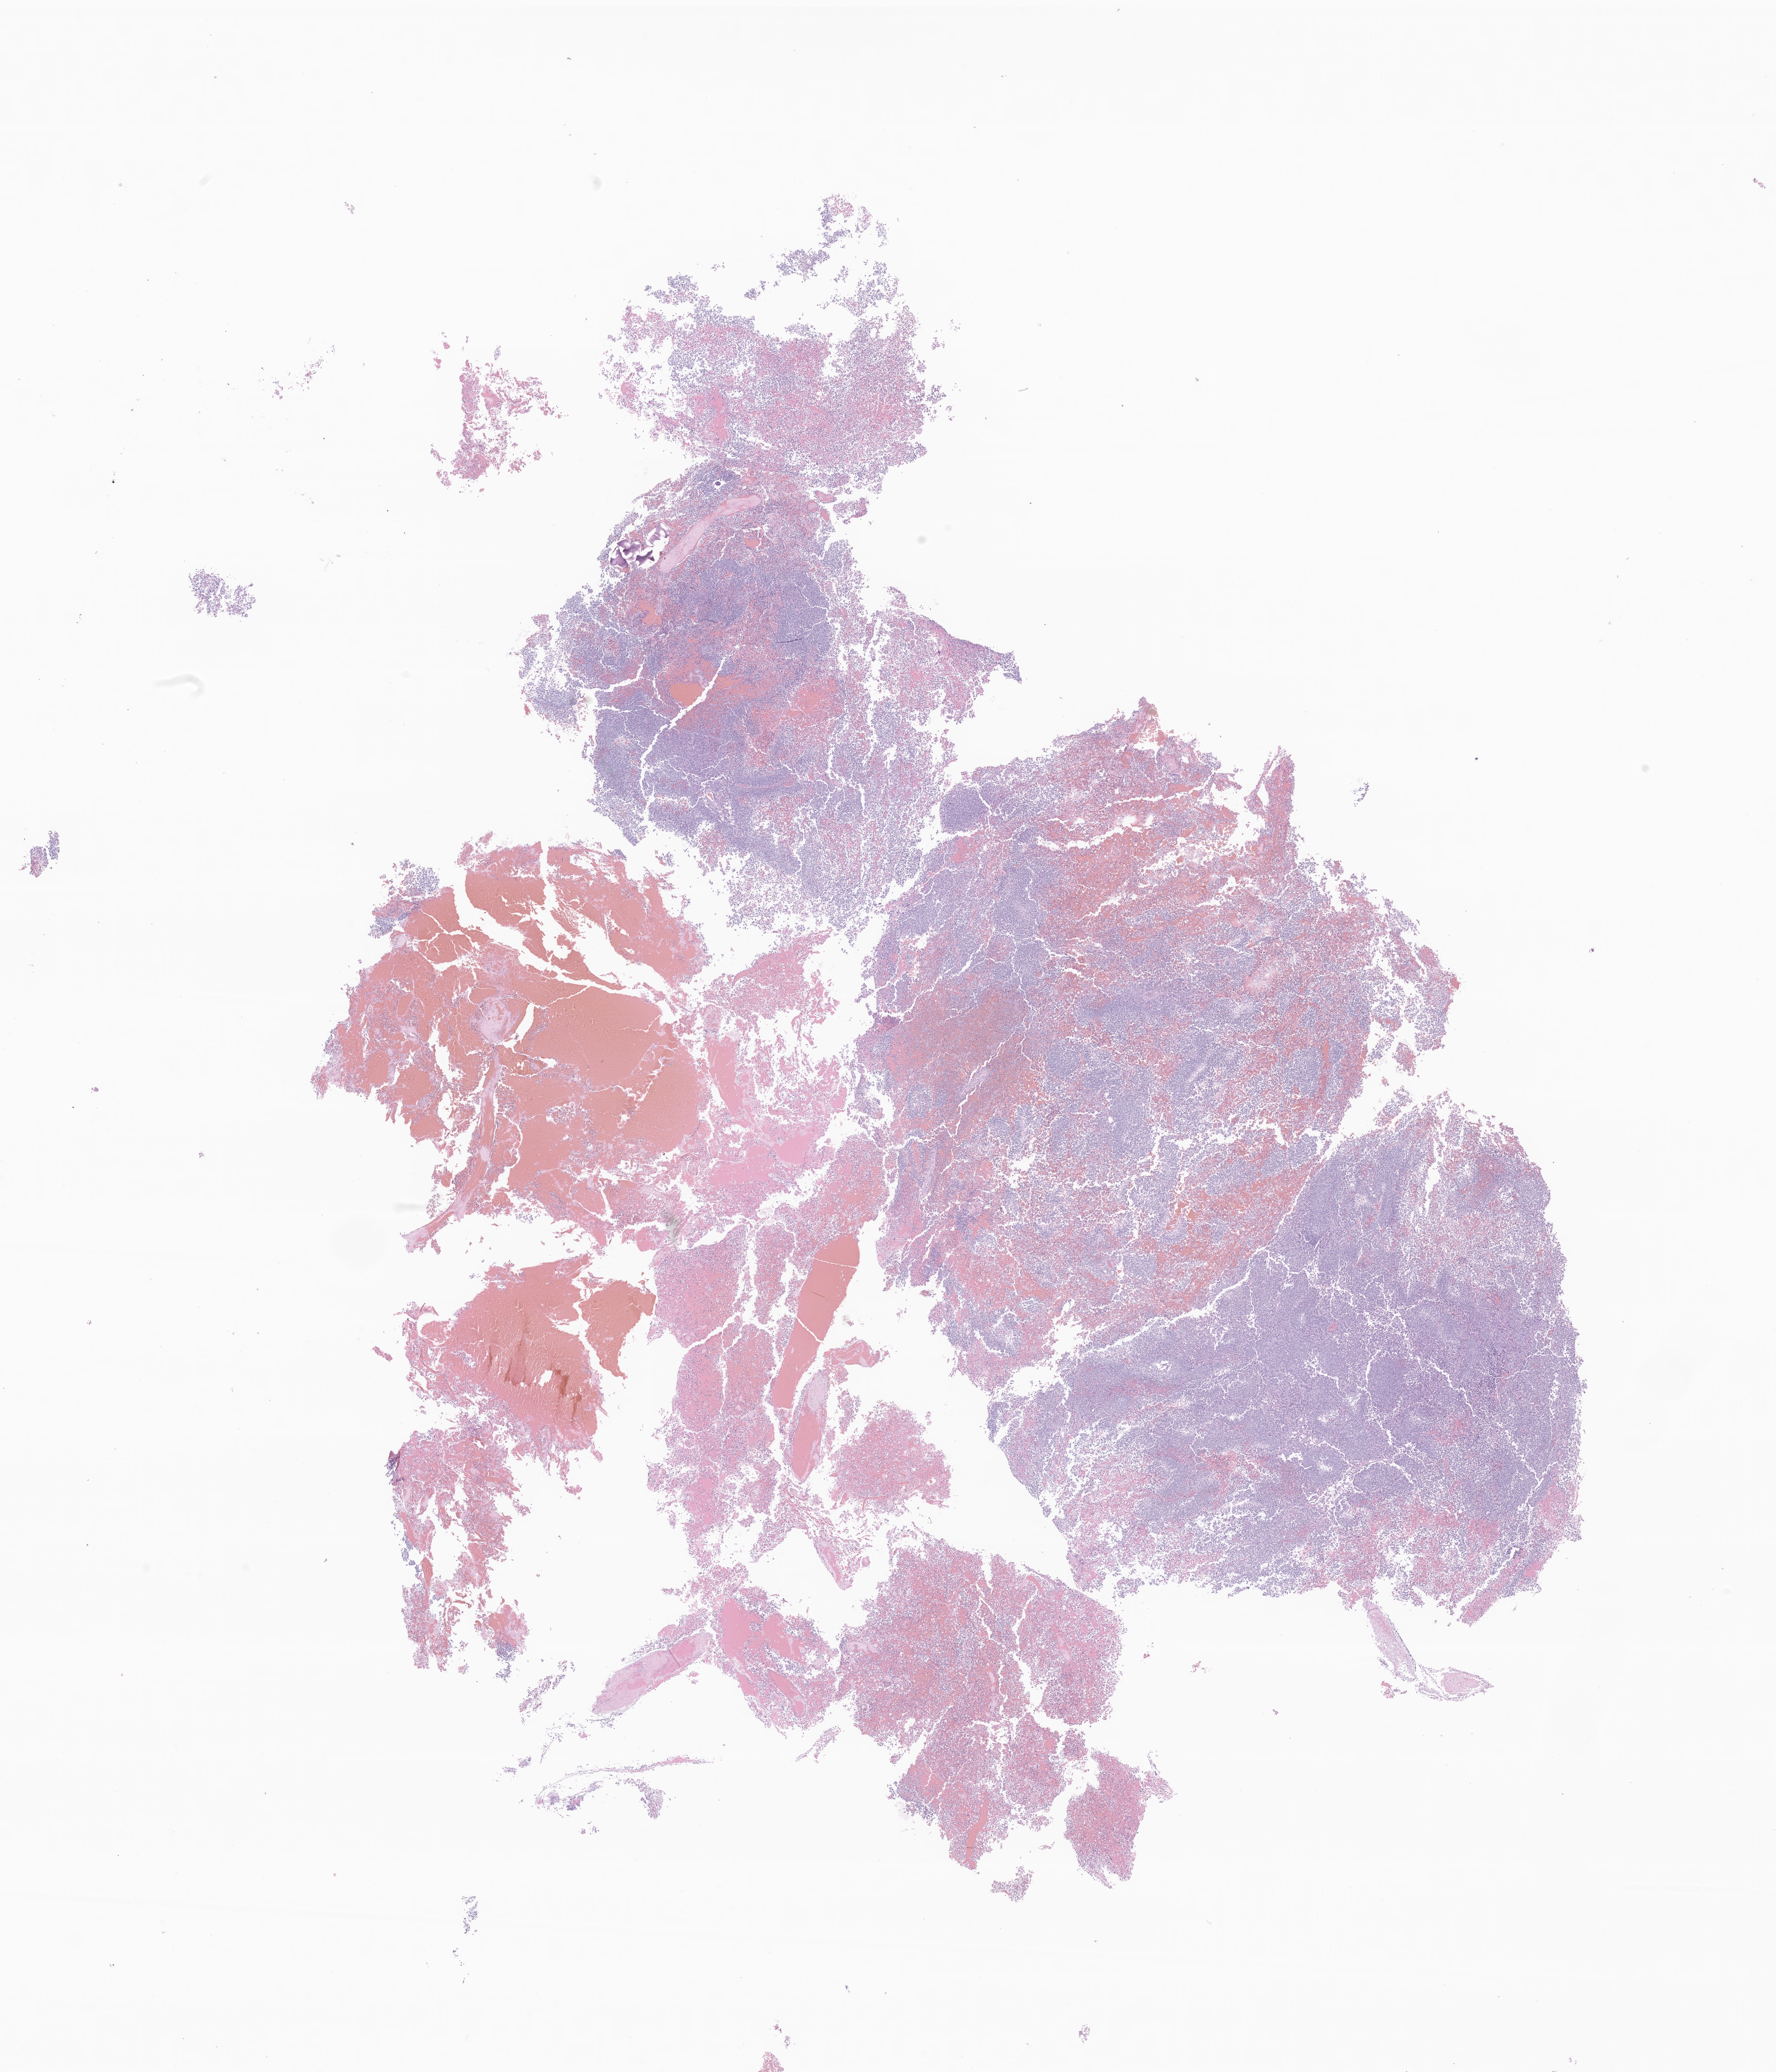
Hematoxylin and eosin (H&E) whole-slide image of tumor tissue from the frontal lobe, a low-resolution overview of the entire scanned area, about 17.5 x 20.4 mm. Formalin-fixed, paraffin-embedded (FFPE) tissue. Patient: female, age 165 months (13 years 9 months).
* diagnosis (ICD-O-3 morphology term): Neoplasm, malignant